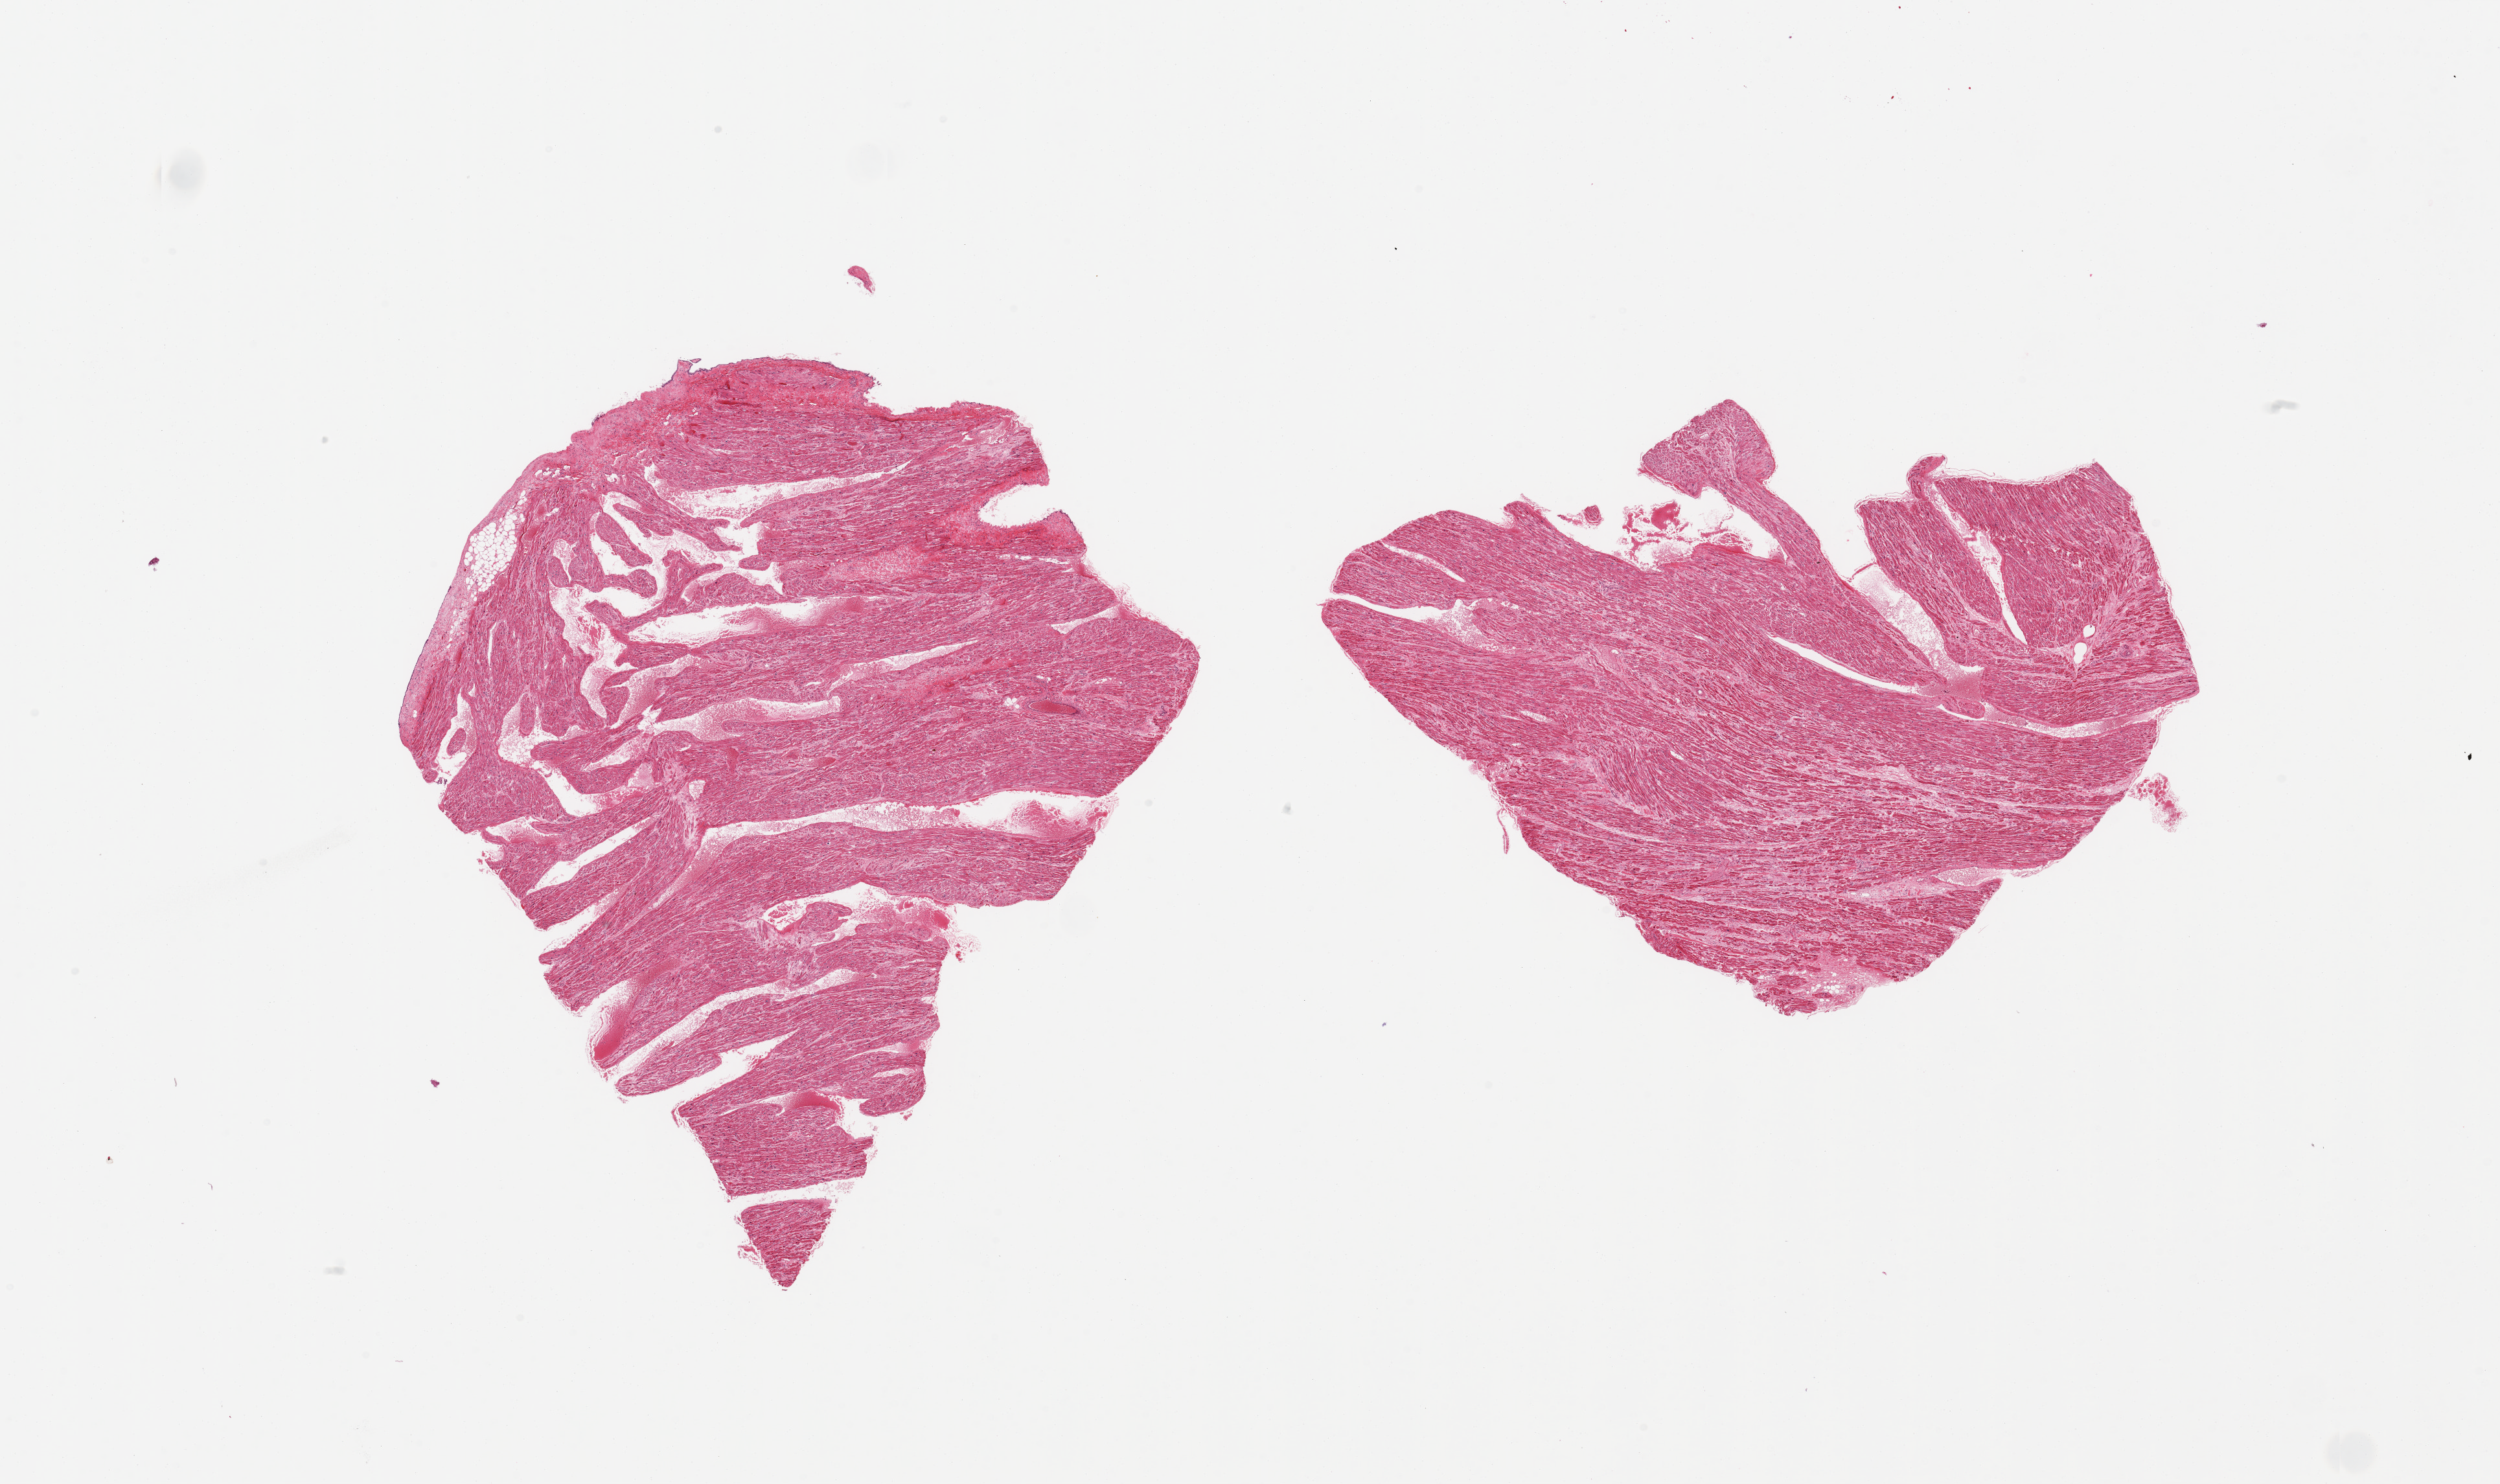
Whole-slide image, hematoxylin and eosin (H&E) stain — low-resolution overview of the scanned area, about 30.5 x 18.1 mm, PAXgene-fixed paraffin-embedded (PFPE) section, section of auricular appendage (target tissue), tissue donor sample. Donor: male.
Reviewer comment on this tissue sample: 2 pieces, no abnormalities.